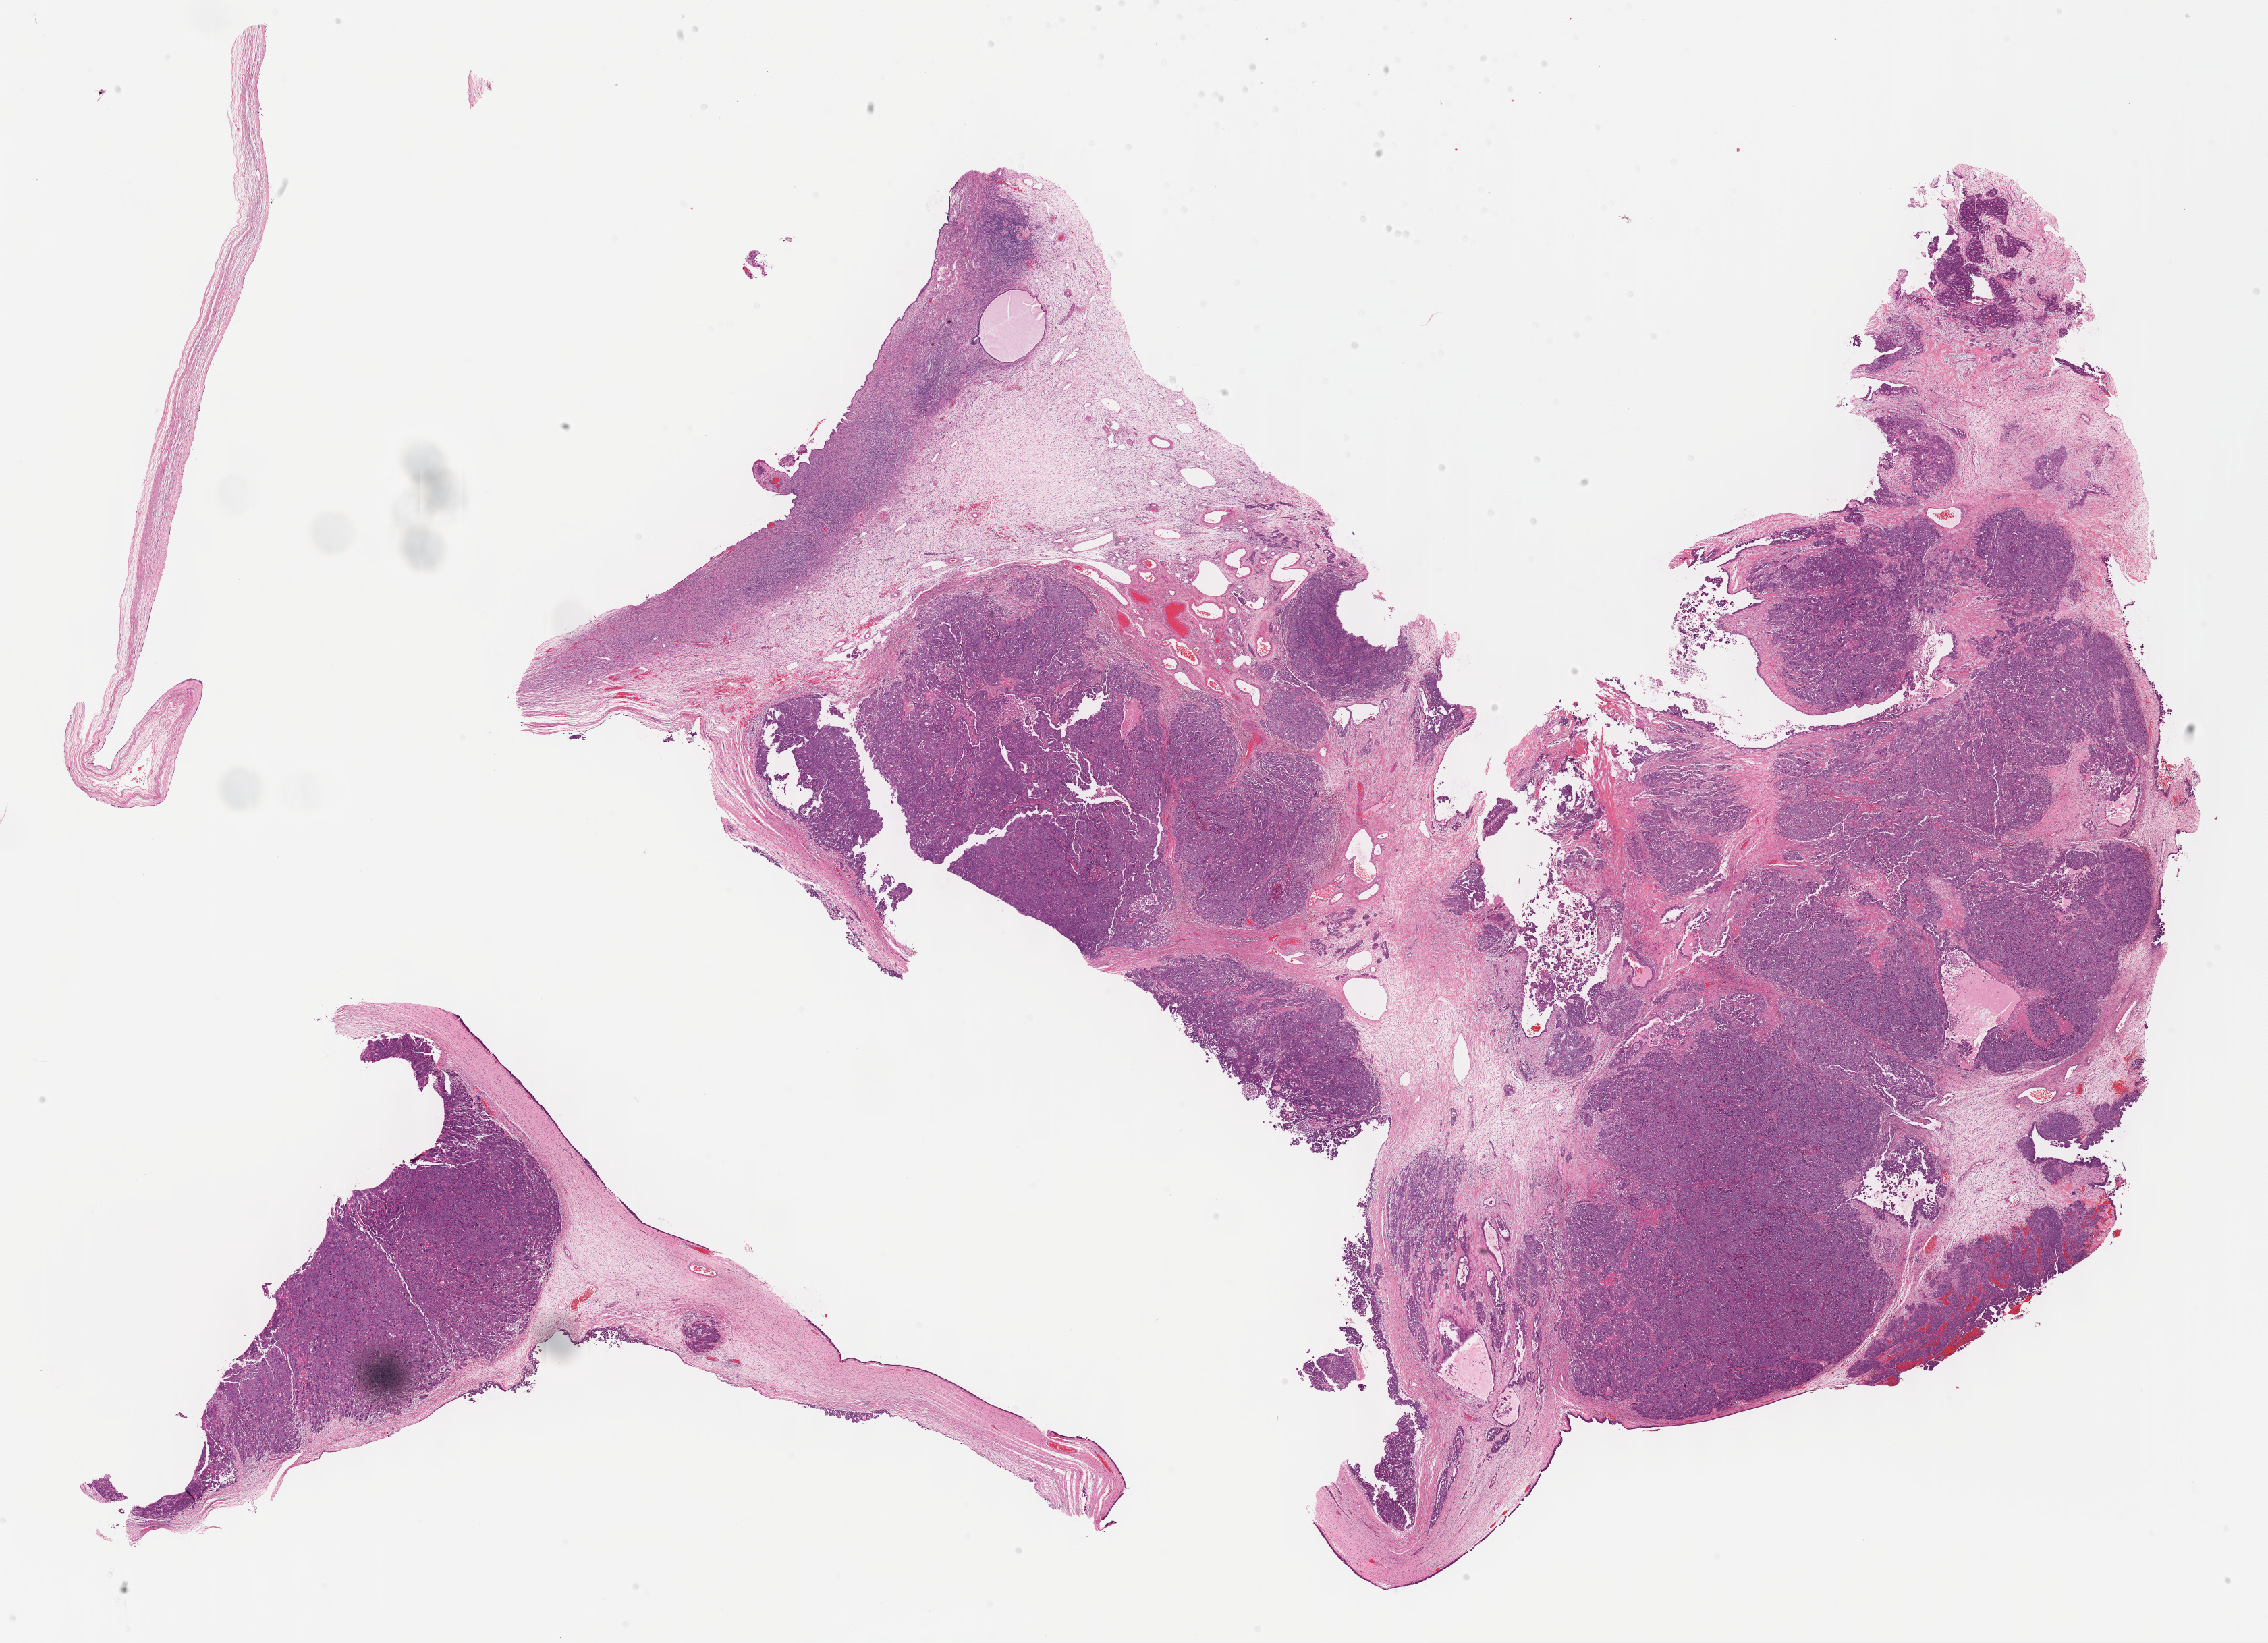
Digitized H&E tissue section (whole slide) — shown as a low-resolution overview of the whole scanned area (about 27.2 x 19.7 mm). Formalin-fixed paraffin-embedded (FFPE) diagnostic section. Primary tumour sample from the ovary. Female, age 60 years at initial diagnosis. Histologic grade: G3 (poorly differentiated).
* FIGO stage: IIIC
* diagnosis: Serous cystadenocarcinoma, NOS
* laterality: left